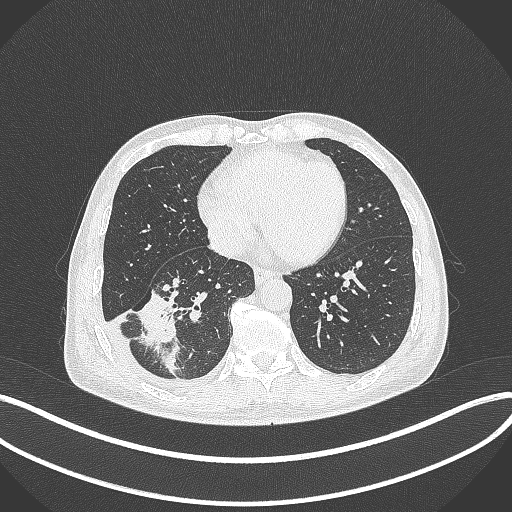
Chest CT, one axial slice. Slice 134 of 388 in the series (ordered by position). Lung window (W 1500 / L -600 HU). 512 × 512 image matrix, field of view 400 × 400 mm. Male patient, age 64 years. Case-level facts recorded for this patient, not image findings: clinical TNM (as recorded): T3 N0 M0.
Structures marked on this image (bounding box drawn by a radiologist):
- lung tumour (recorded histology: adenocarcinoma): bounding box [x1, y1, x2, y2] px = [139, 286, 183, 377]